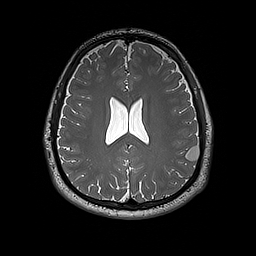
Brain MRI from a brain-tumour surgery series, one axial slice; position 78 of 192 along the scan axis; 256 × 256 image matrix, field of view 250 × 250 mm. Case-level facts recorded for this patient, not image findings: histopathology: Dysembryoplastic neuroepithelial tumor; WHO grade: 1; IDH mutation: no; tumour location: Left Inferior Parietal.
Outlined on this slice (expert manual segmentation):
- tumour: bounding box <185,146,200,161> (left, top, right, bottom; pixels)